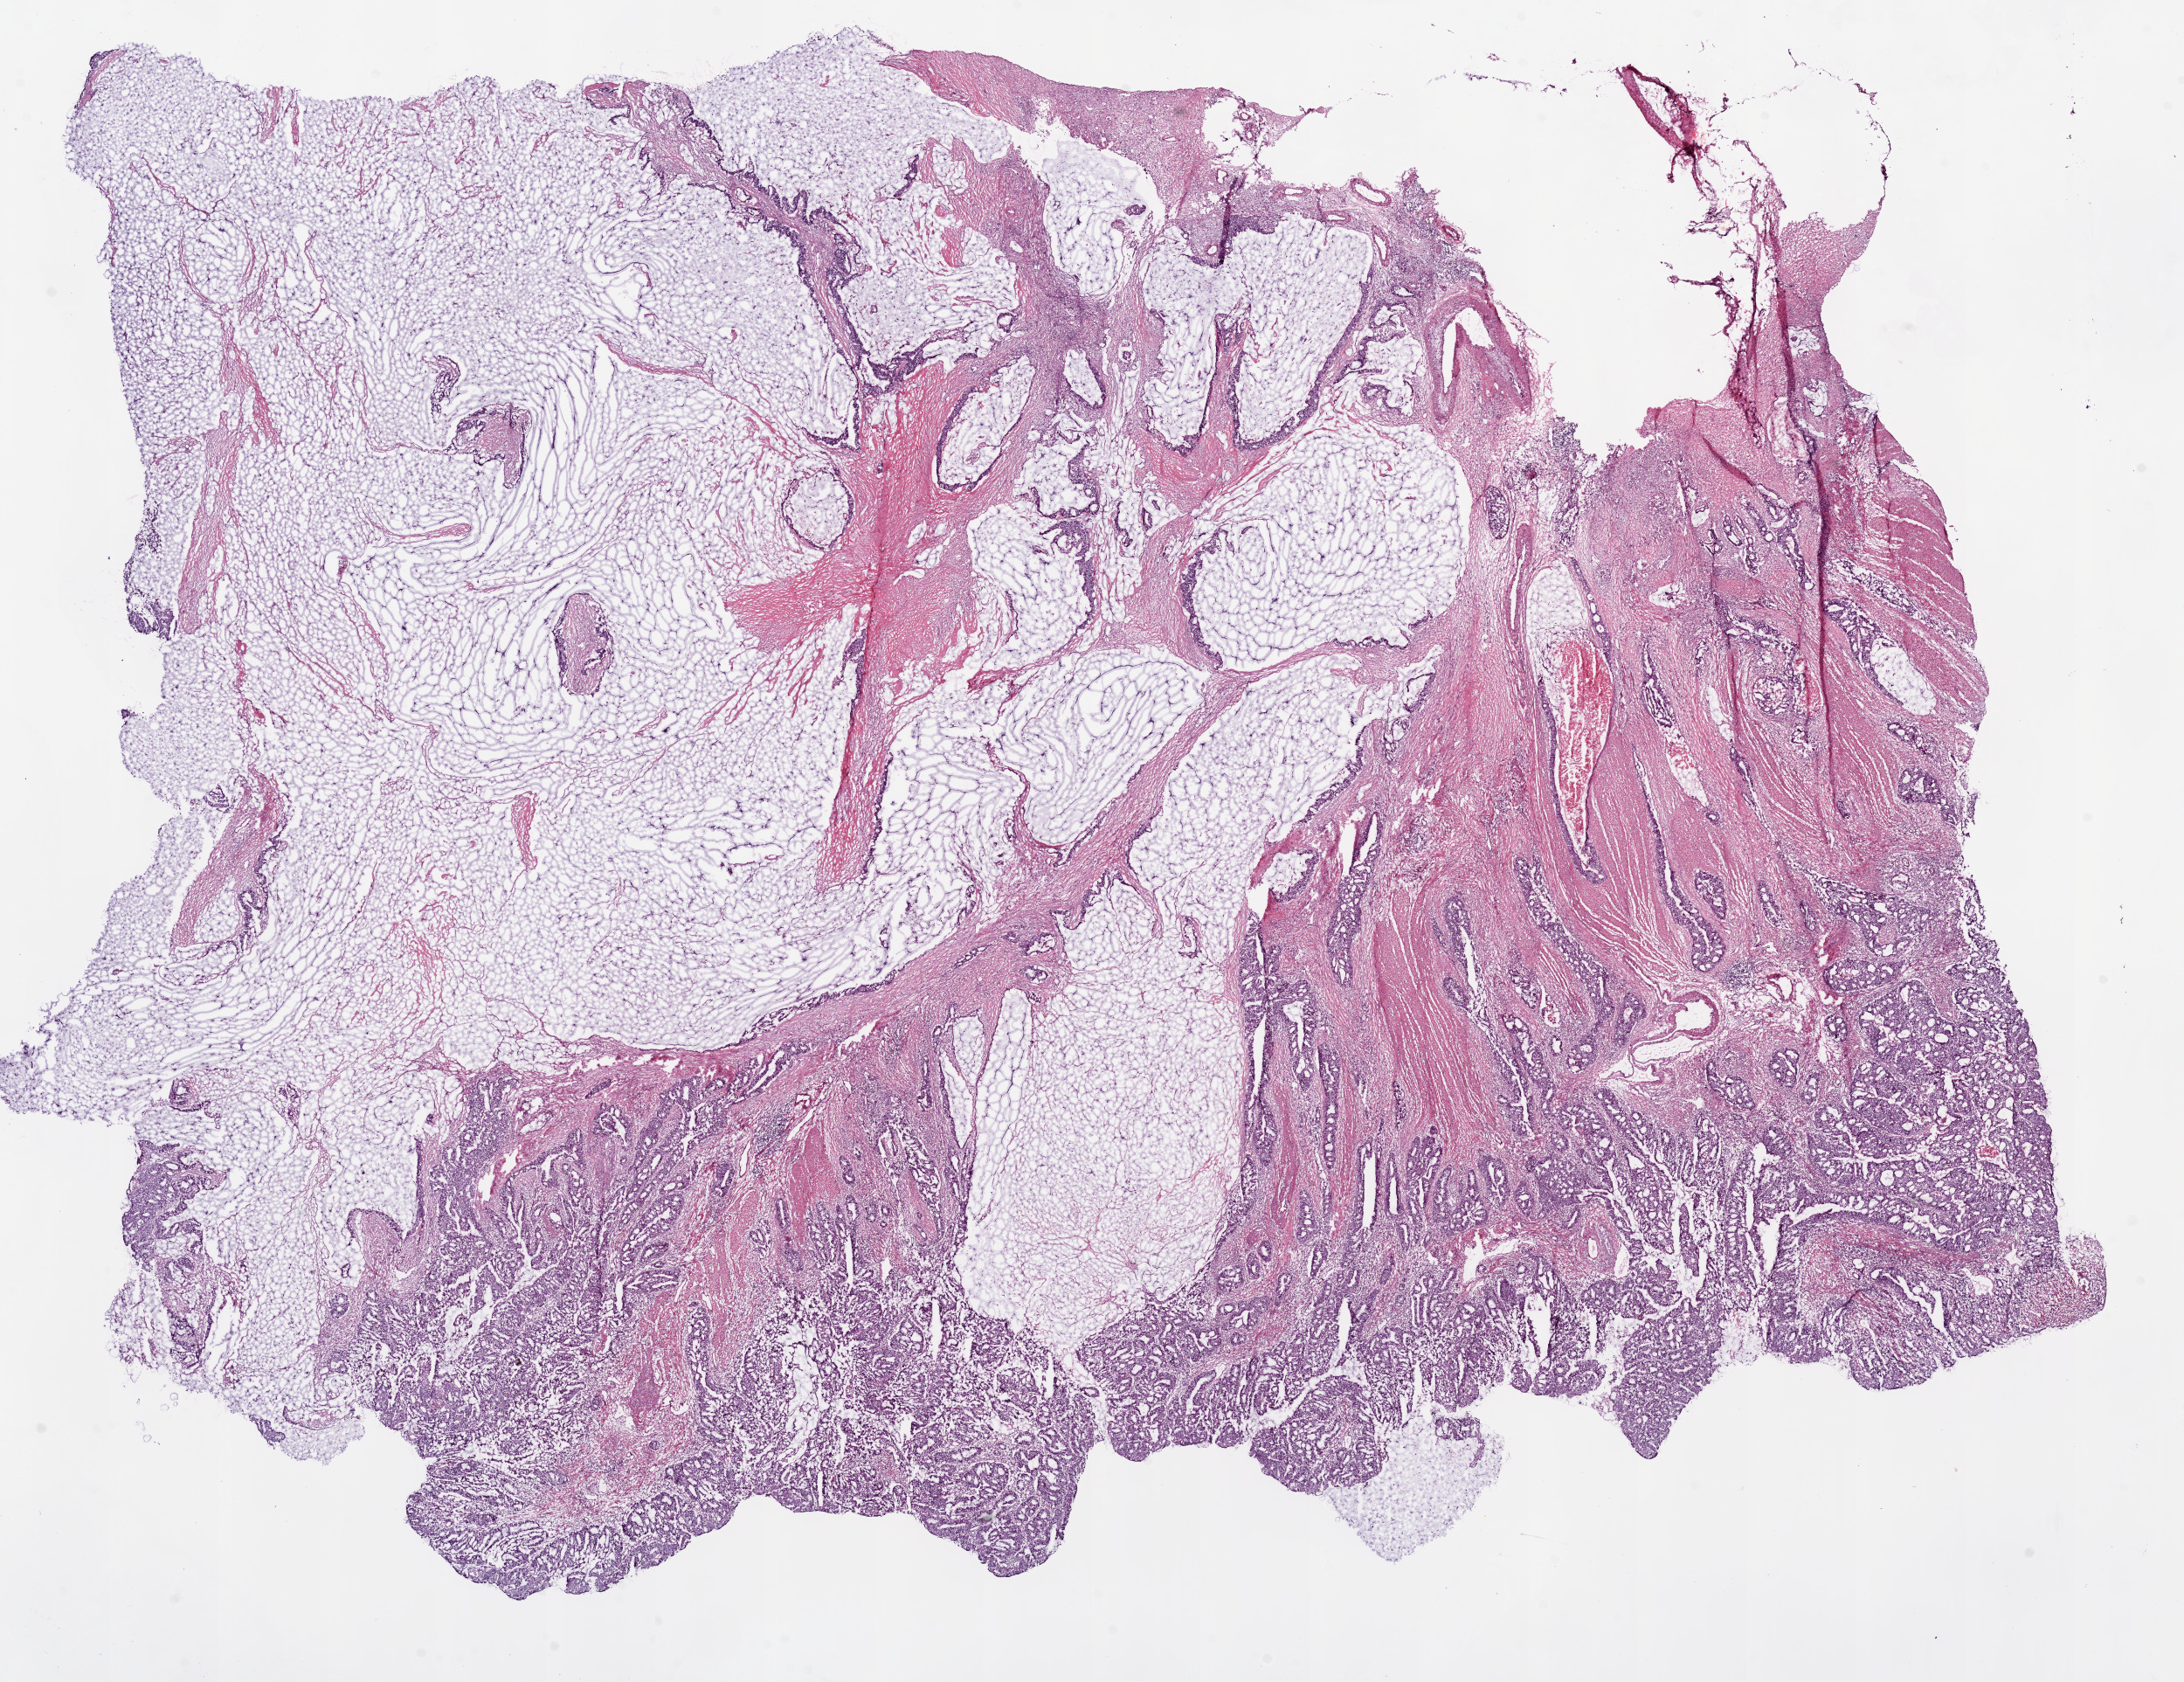
Whole-slide histology image, H&E, low-resolution overview of the scanned area, about 20.1 x 15.4 mm (from a 20x scan), frozen section from the bottom of the tissue portion, sample: primary tumour, colon. Male patient; age at initial diagnosis 53 years. Slide review estimates, as recorded: tumour cells 82%, tumour nuclei 75%, normal cells 1%, stromal cells 15%, necrosis 2%.
AJCC pathologic stage: IIIB. TNM: T4a N1a M0. Histologic diagnosis: Mucinous adenocarcinoma (transverse colon).